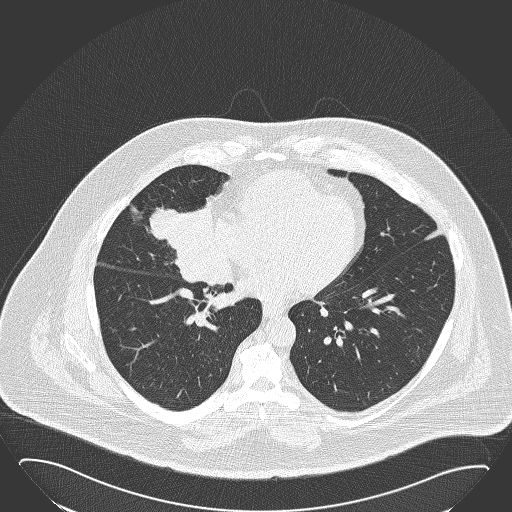
Low-dose screening chest CT, one axial slice. Position 72 of 168 along the scan axis. Reconstruction kernel B50f. Lung window (W 1500 / L -600 HU). 2 mm slice thickness. 512 × 512 image matrix, field of view 432 × 432 mm.
Structures marked on this image (manually delineated by an expert):
- lesion 1 (tumor, hilum of right lung): box from (x=149, y=206) to (x=229, y=286) px